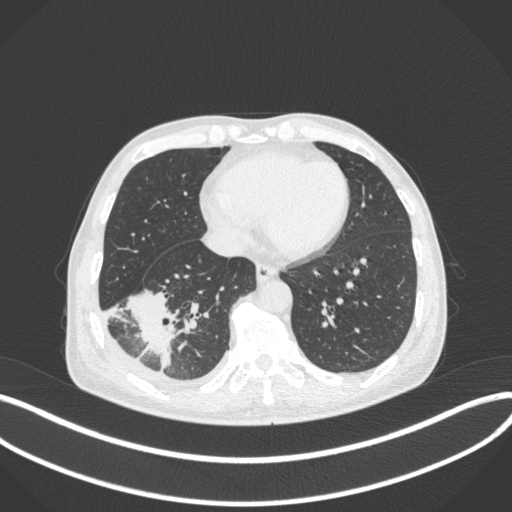
Chest CT, one axial slice. Lung window (W 1500 / L -600 HU). 1 mm slice thickness. 512 × 512 image matrix. Patient: male, 64 years. From the clinical record (not read from this slice): clinical TNM (as recorded): T3 N0 M0.
Structures marked on this image (bounding box drawn by a radiologist):
- lung tumour (recorded histology: adenocarcinoma): bounding box [x1, y1, x2, y2] px = [120, 284, 175, 371]